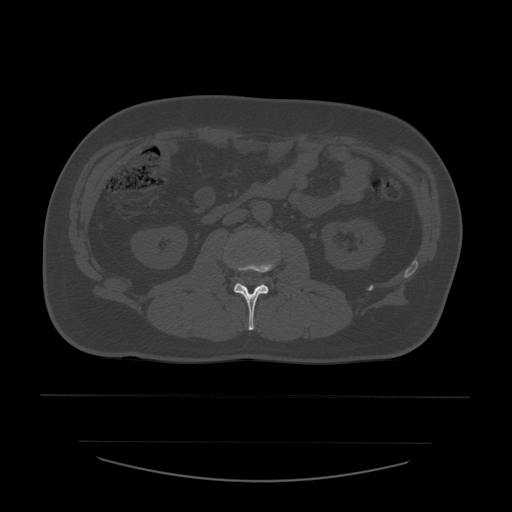
CT including the spine, one axial slice; position 191 of 532 along the scan axis; bone window (W 1800 / L 400 HU); 1.25 mm slice thickness; 512 × 512 image matrix, field of view 441 × 441 mm. Patient age 44 years. Case-level facts recorded for this patient, not image findings: primary cancer: soft tissue sarcoma.
Structures marked on this image (semi-automatic segmentation, software-assisted and operator-edited):
- L2 vertebra: bounding box [x1, y1, x2, y2] px = [232, 260, 277, 331]